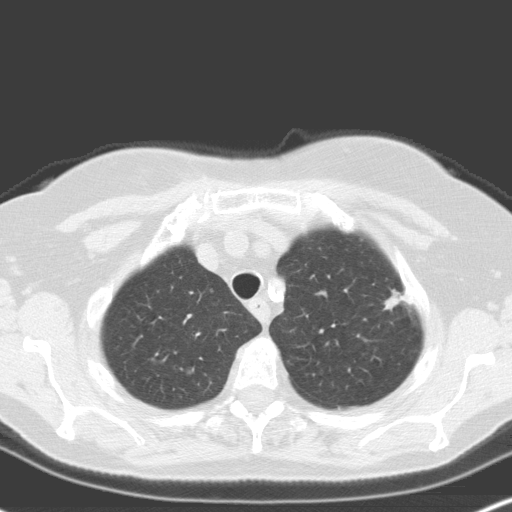
Low-dose screening chest CT, one axial slice; position 139 of 160 along the scan axis; 120 kVp; lung window (W 1500 / L -600 HU); 3.2 mm slice thickness; 512 × 512 image matrix, field of view 316 × 316 mm.
Outlined on this slice (expert manual segmentation):
- lesion 2 (nodule): bounding box [x1, y1, x2, y2] px = [384, 291, 412, 310]